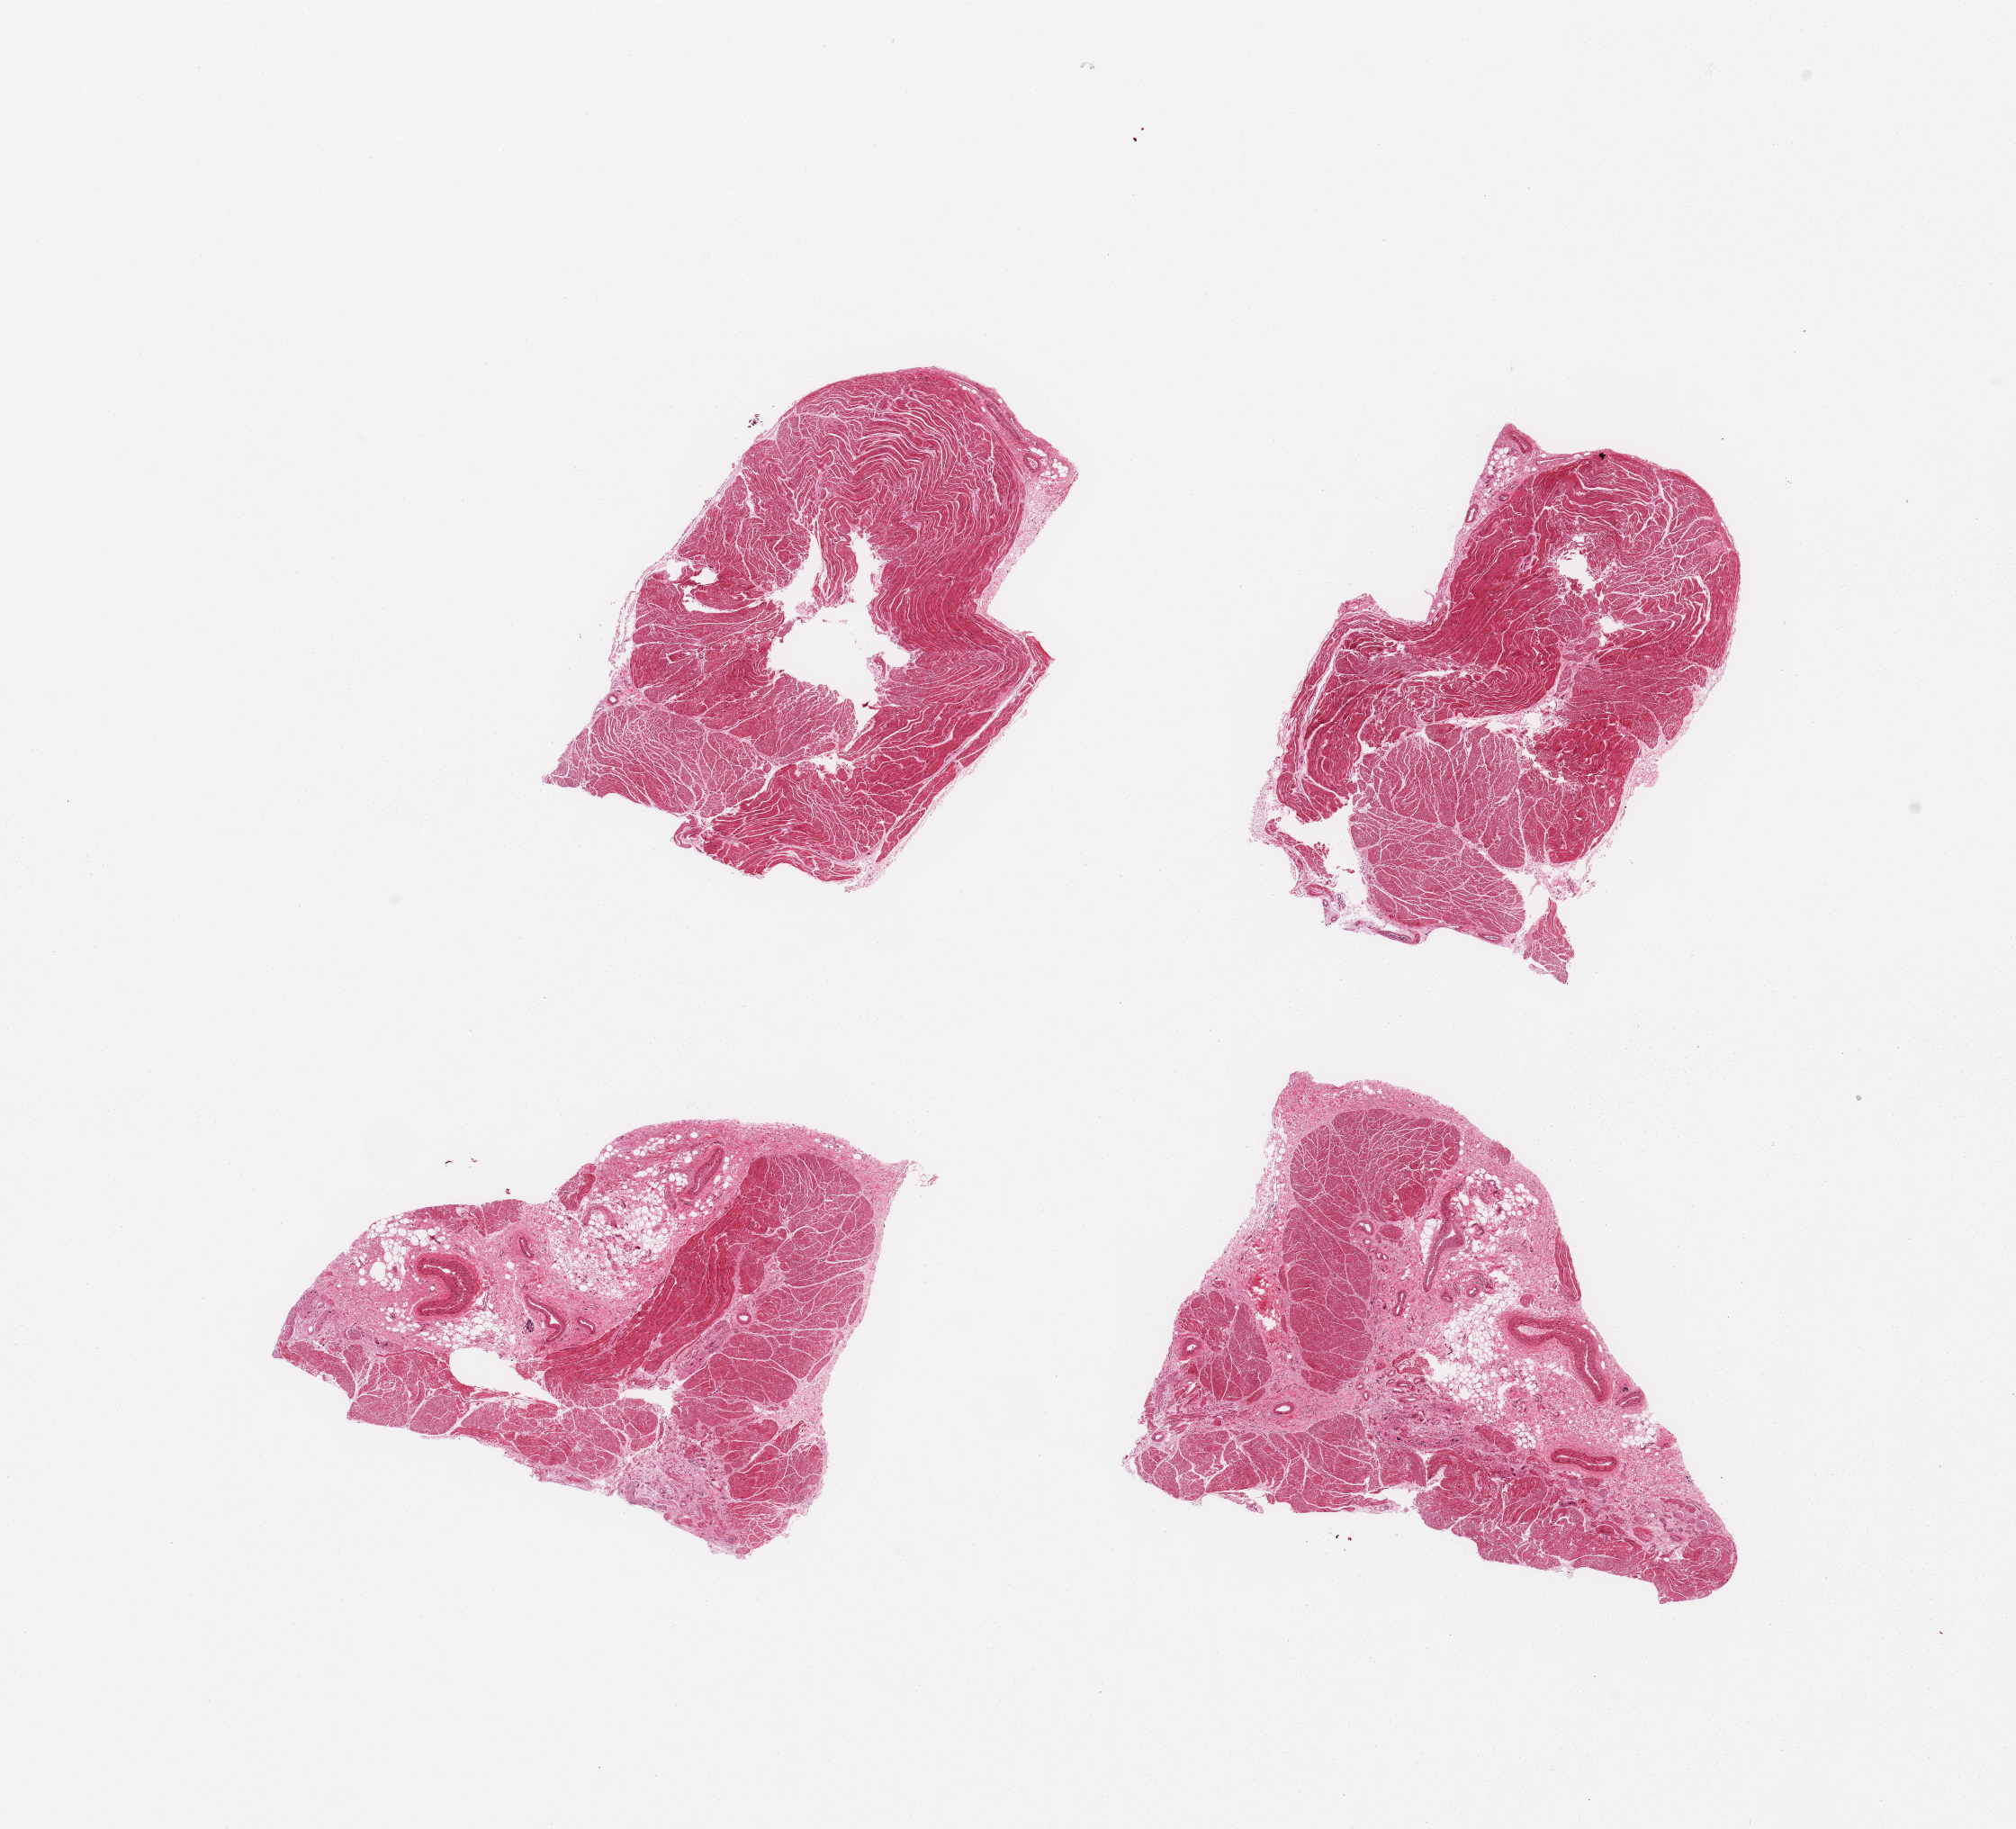
Whole-slide image, H&E stain, low-resolution overview of the scanned area, about 17.7 x 16.1 mm (from a 20x scan), PAXgene-fixed paraffin-embedded (PFPE) section, target tissue: esophageal muscle, tissue donor sample. Donor: male.
Review note (as recorded): 4 pieces; 2 contain 50% fibrofatty stroma.